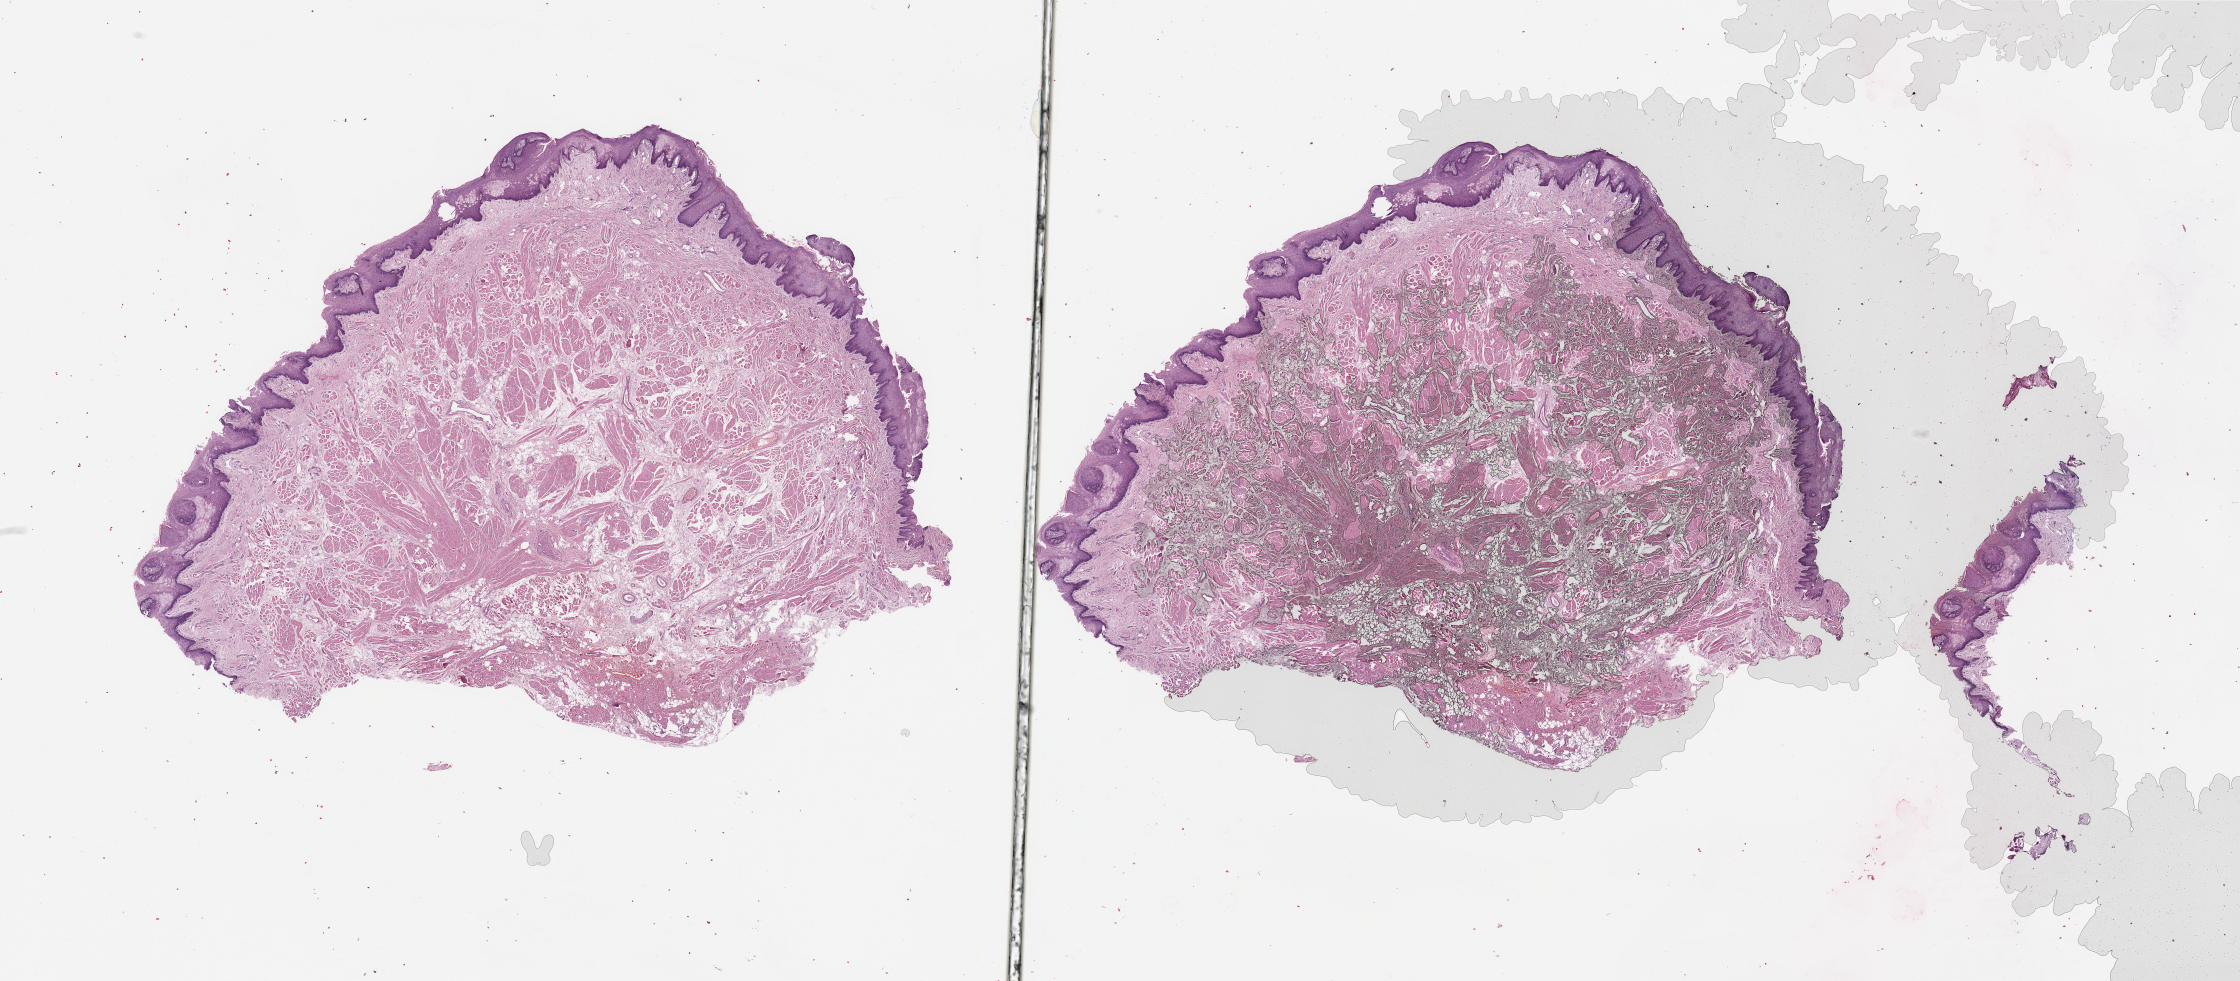
H&E-stained whole-slide image — shown as a low-resolution overview of the whole scanned area (about 35.4 x 15.5 mm), normal (non-tumour) tissue sample, sampled site: tongue. Male, 23 y/o.
This section: normal (non-tumour) tissue from the same patient. Patient diagnosis: Squamous cell carcinoma, NOS (tongue, NOS).